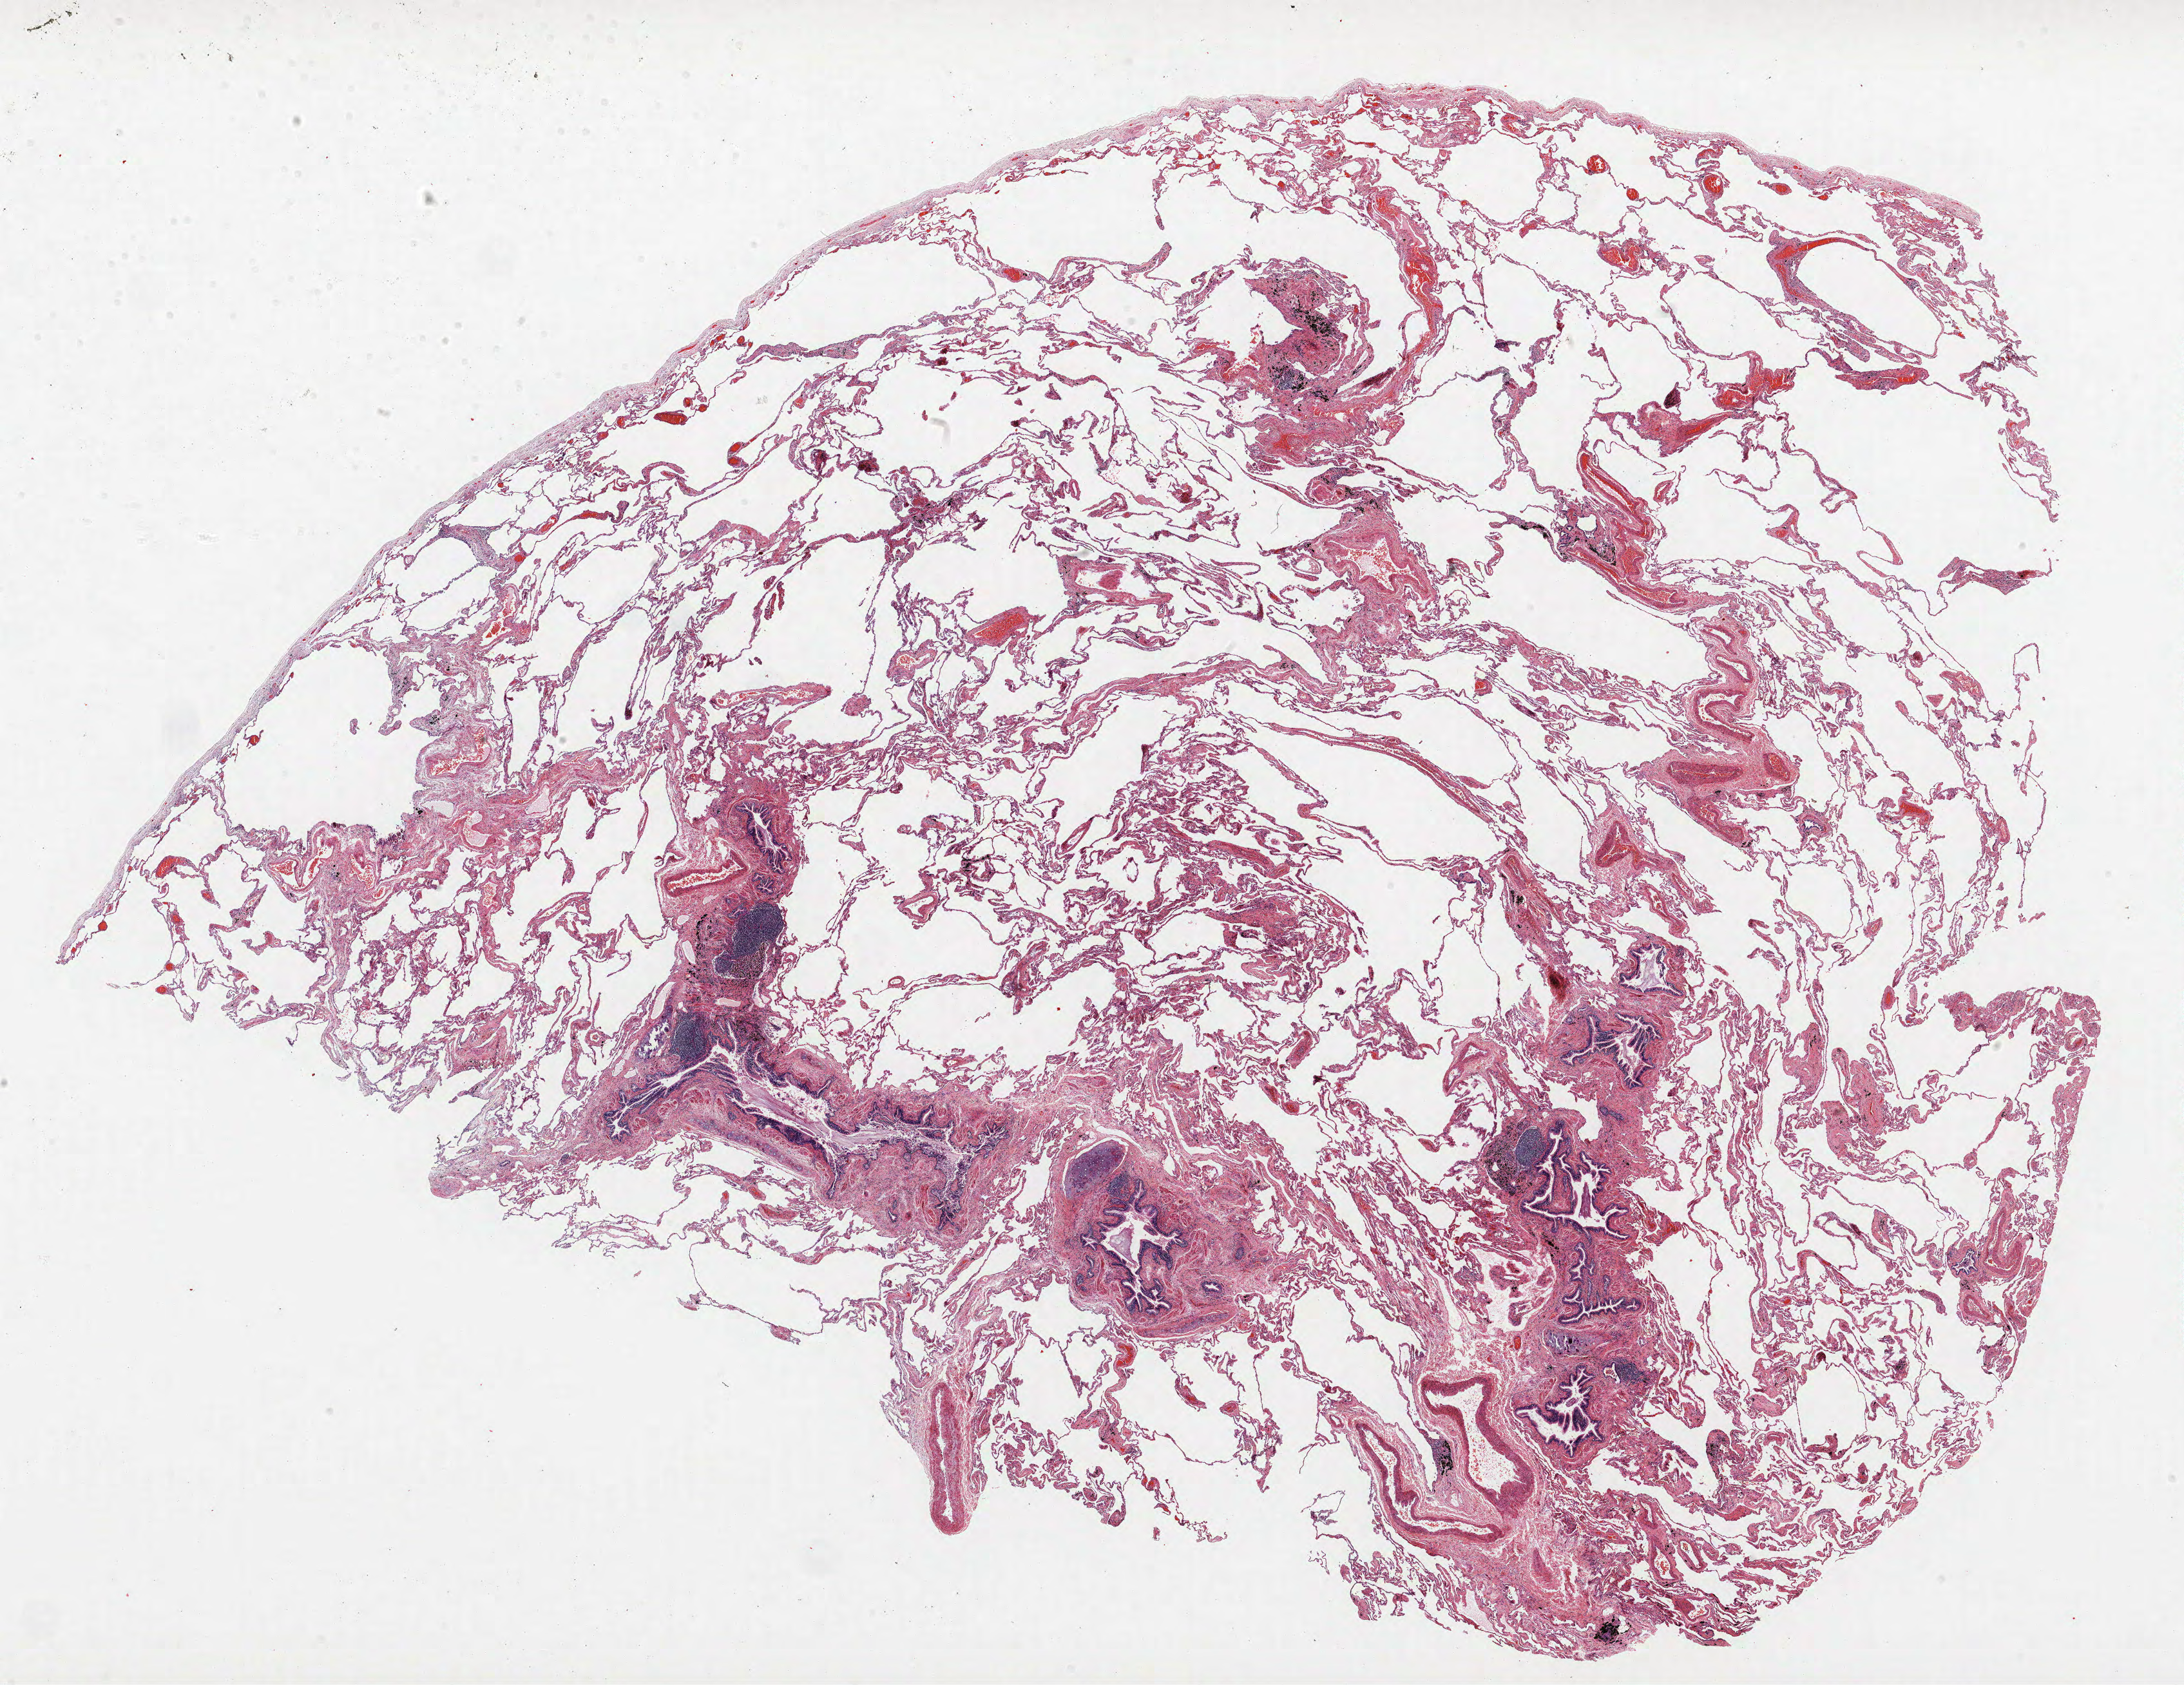
Whole-slide histology image, Hematoxylin and eosin (H&E) stained — shown as a low-resolution overview of the whole scanned area (about 27.1 x 20.9 mm), FFPE section, lung tissue. Male patient, aged 65 at enrolment. Former smoker at enrolment. Grade: moderately differentiated (G2).
* primary tumour location (clinical record): right upper lobe
* ICD-O-3 topography: upper lobe of lung (C34.1)
* stage (AJCC 6th edition): IIA
* participant's lung-cancer diagnosis: Bronchiolo-alveolar adenocarcinoma, NOS (ICD-O-3 8250/3)
* tumour size (pathology): 14 mm